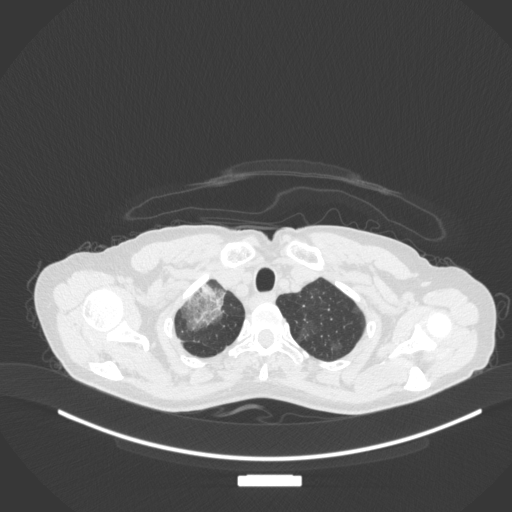
Chest CT, one axial slice. Reconstruction kernel B31f. Lung window (W 1500 / L -600 HU). 512 × 512 image matrix, field of view 400 × 400 mm. Female patient, age 59 years. Case-level facts recorded for this patient, not image findings: clinical TNM (as recorded): T3 N0 M0.
Annotated regions visible in this slice (bounding box drawn by a radiologist):
- lung tumour (recorded histology: adenocarcinoma): bounding box [x1, y1, x2, y2] px = [176, 279, 233, 331]